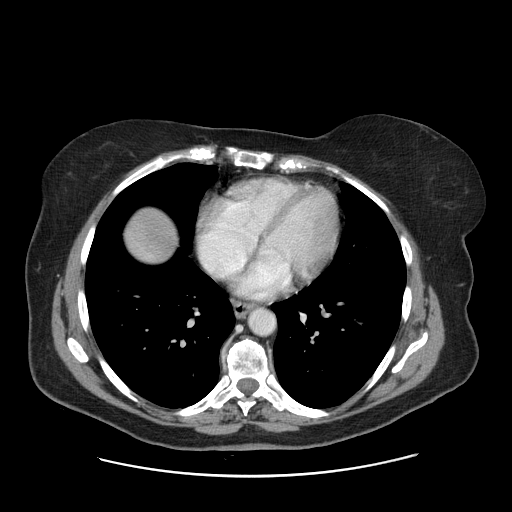
Contrast-enhanced abdominal CT, one axial slice. Position 154 of 161 along the scan axis. Intravenous contrast given. Soft-tissue window (W 400 / L 40 HU). 2.5 mm slice thickness. 512 × 512 image matrix. Female patient, age 62 years. Case-level facts recorded for this patient, not image findings: diagnosis: colorectal cancer liver metastases, imaged before liver resection; multiple liver metastases: no; largest metastasis: 2.5 cm; chemotherapy before resection: yes.
Annotated regions visible in this slice (outlined manually by an expert reader):
- liver: bounding box (x1, y1, x2, y2) in pixels: (127, 210, 175, 262)
- planned liver remnant (the part of the liver to remain after resection): (127, 211, 176, 261)